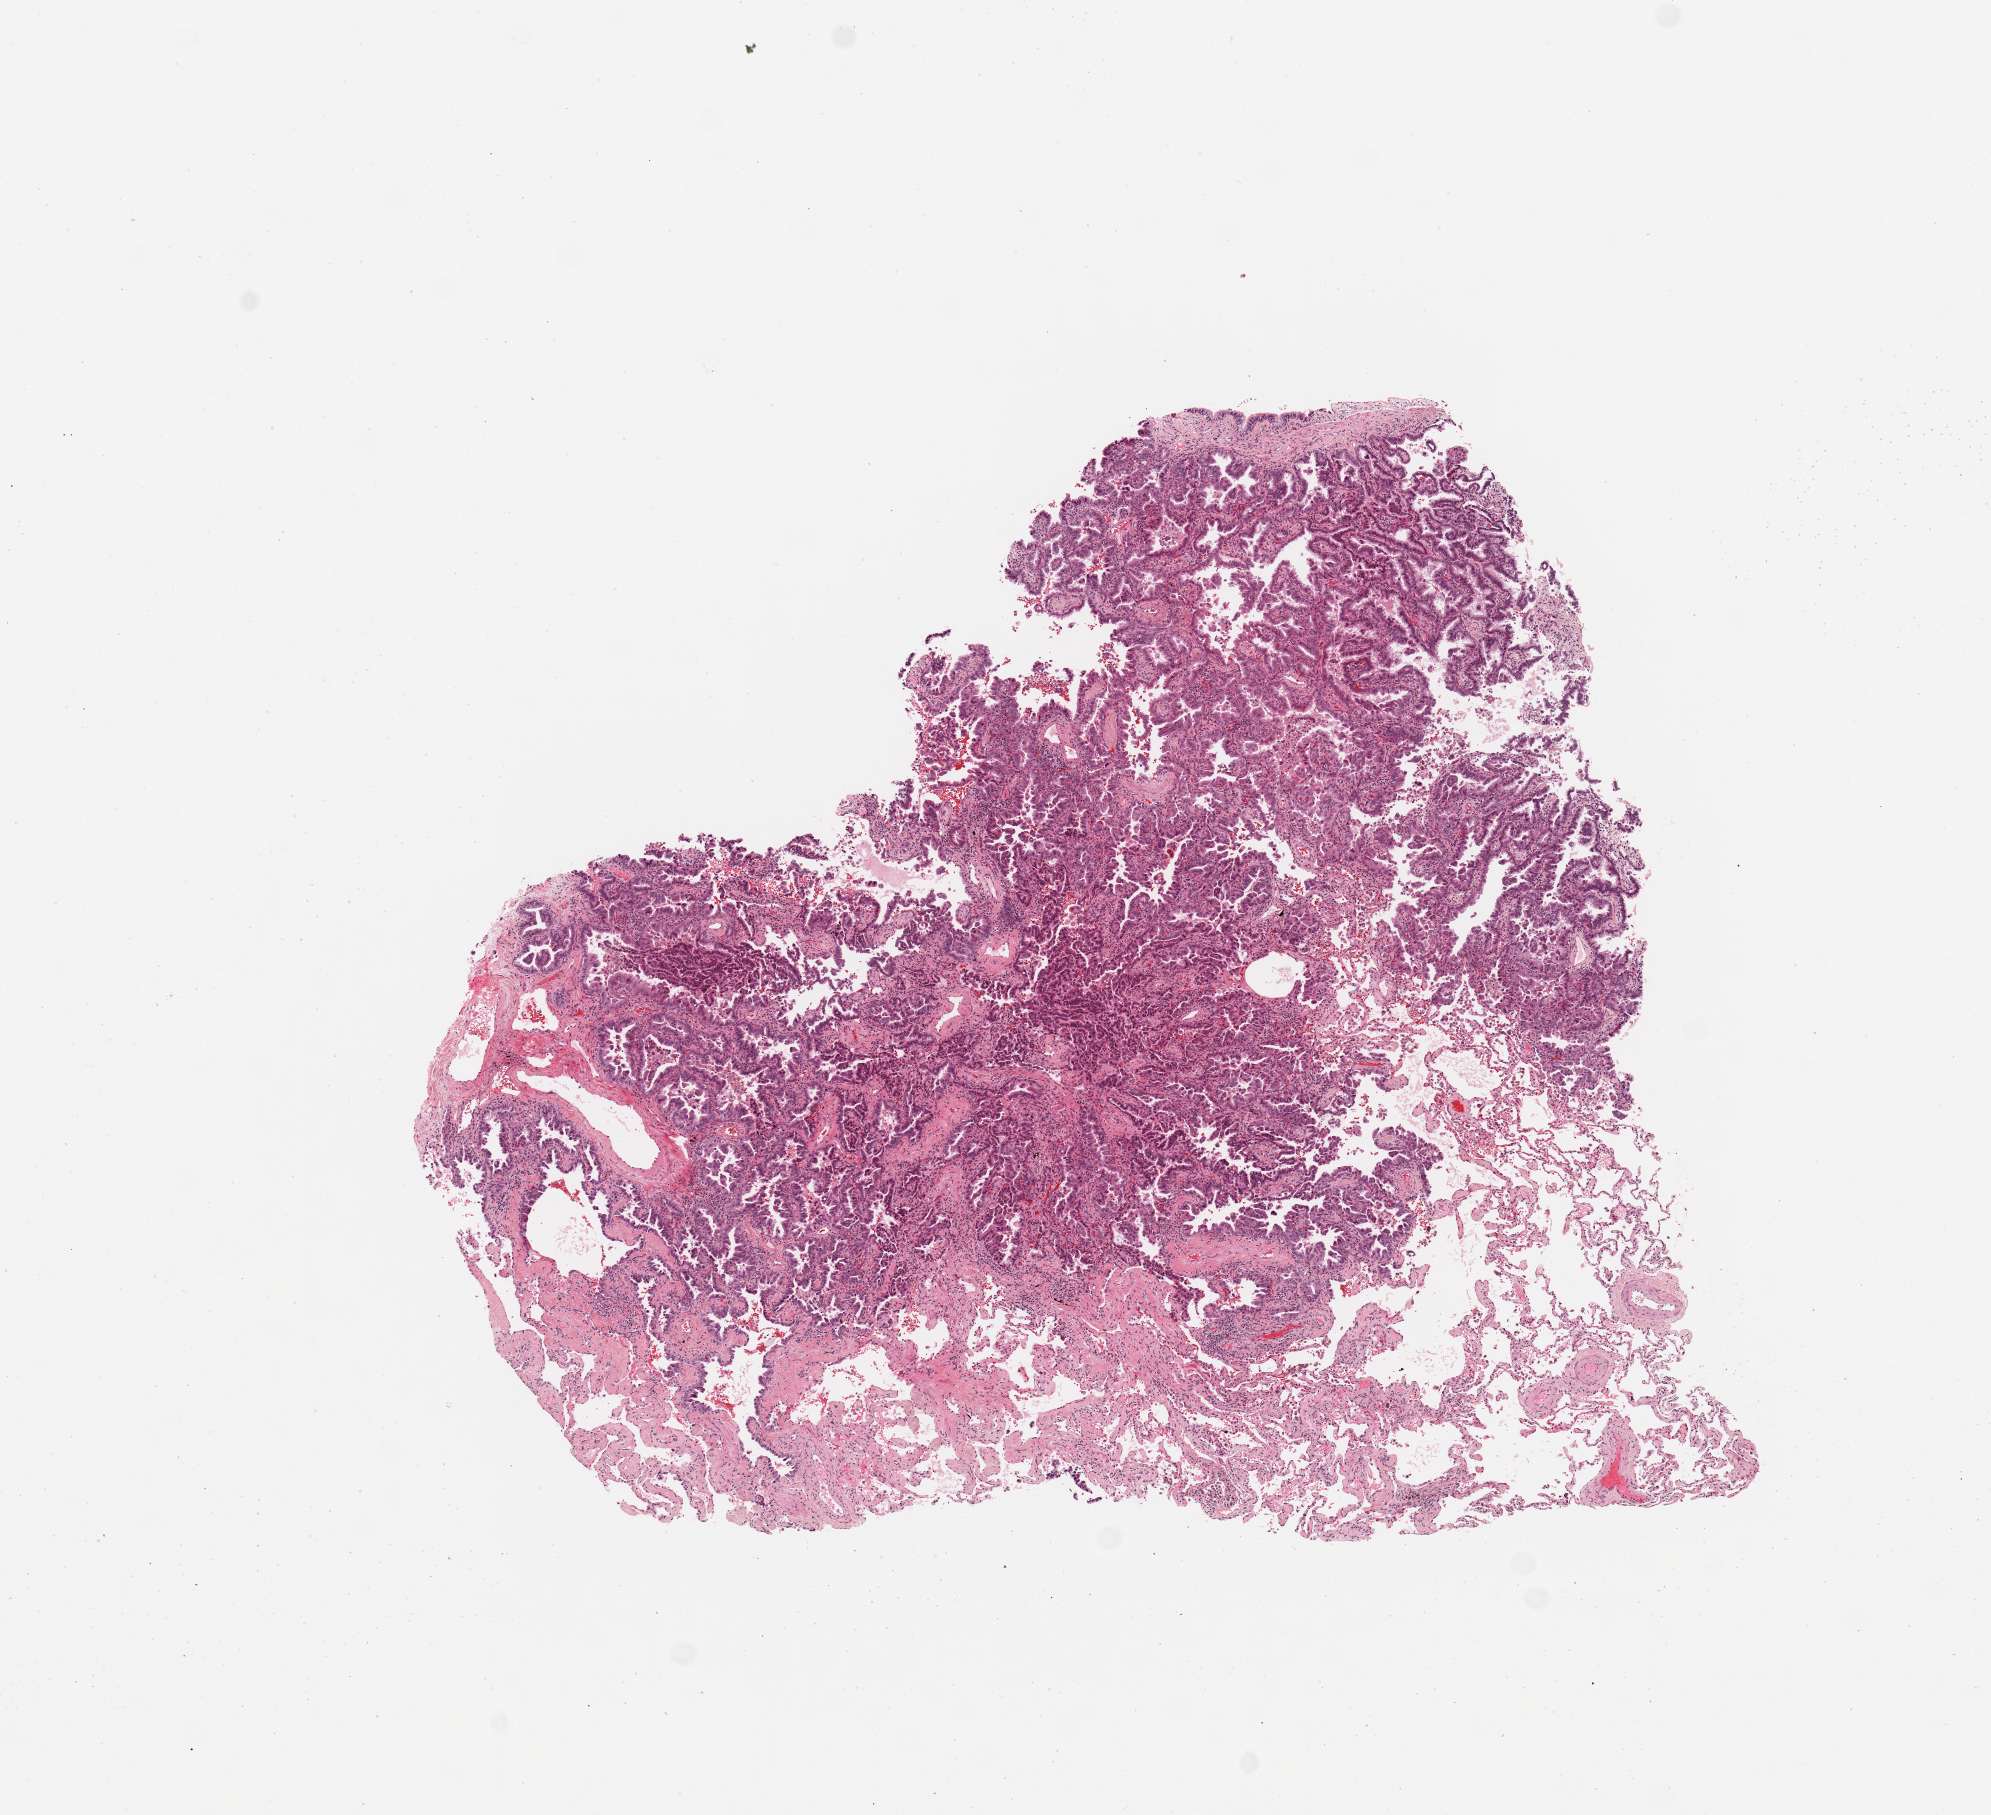
Whole-slide histology image, Hematoxylin and eosin (H&E) stained — a low-resolution overview of the entire scanned area, about 7.9 x 7.2 mm (slide scanned at 20x). Tumour tissue sample, sampled site: lung. Patient: female, age 70 years. Histologic grade: G2 (moderately differentiated). Pathologist review of this section (percent, as recorded): tumour nuclei 60%, necrosis 3%.
Histologic diagnosis: Adenocarcinoma, NOS. AJCC pathologic stage: IA2.